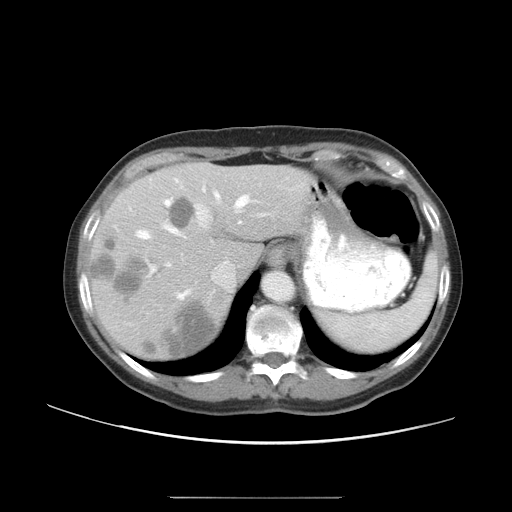
Contrast-enhanced abdominal CT, one axial slice; position 36 of 50 along the scan axis; reconstruction kernel STANDARD; soft-tissue window (W 400 / L 40 HU); 5 mm slice thickness; 512 × 512 image matrix. Female patient, age 58 years. From the clinical record (not read from this slice): diagnosis: colorectal cancer liver metastases, imaged before liver resection; multiple liver metastases: yes; largest metastasis: 7.3 cm; disease in both lobes: yes.
Annotated regions visible in this slice (outlined manually by an expert reader):
- hepatic veins: bounding box <137,187,252,299> (left, top, right, bottom; pixels)
- liver: <94,164,306,359>
- planned liver remnant (the part of the liver to remain after resection): <175,164,306,272>
- portal vein (with intrahepatic branches): <151,183,211,272>
- liver metastasis: <144,304,216,356>
- liver metastasis: <171,199,195,229>
- liver metastasis: <90,236,147,297>